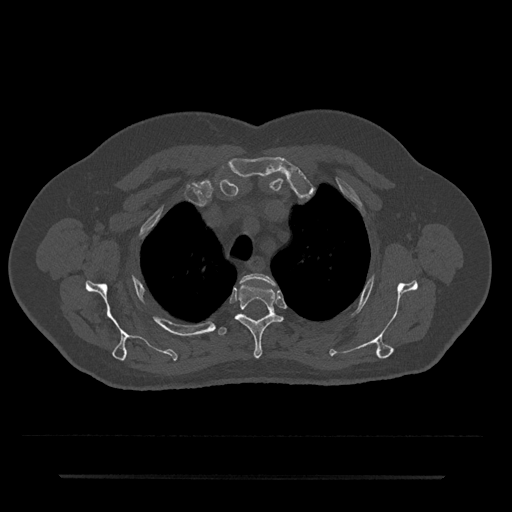
CT including the spine, one axial slice; position 566 of 797 along the scan axis; 120 kVp; bone window (W 1800 / L 400 HU); 0.5 mm slice thickness; 512 × 512 image matrix, field of view 437 × 437 mm. Patient: male, 69 years. From the clinical record (not read from this slice): primary cancer: prostate.
Structures marked on this image (semi-automatic segmentation, software-assisted and operator-edited):
- T2 vertebra: bounding box [x1, y1, x2, y2] px = [241, 273, 275, 285]
- T3 vertebra: [234, 283, 283, 359]
- T4 vertebra: [218, 327, 227, 336]